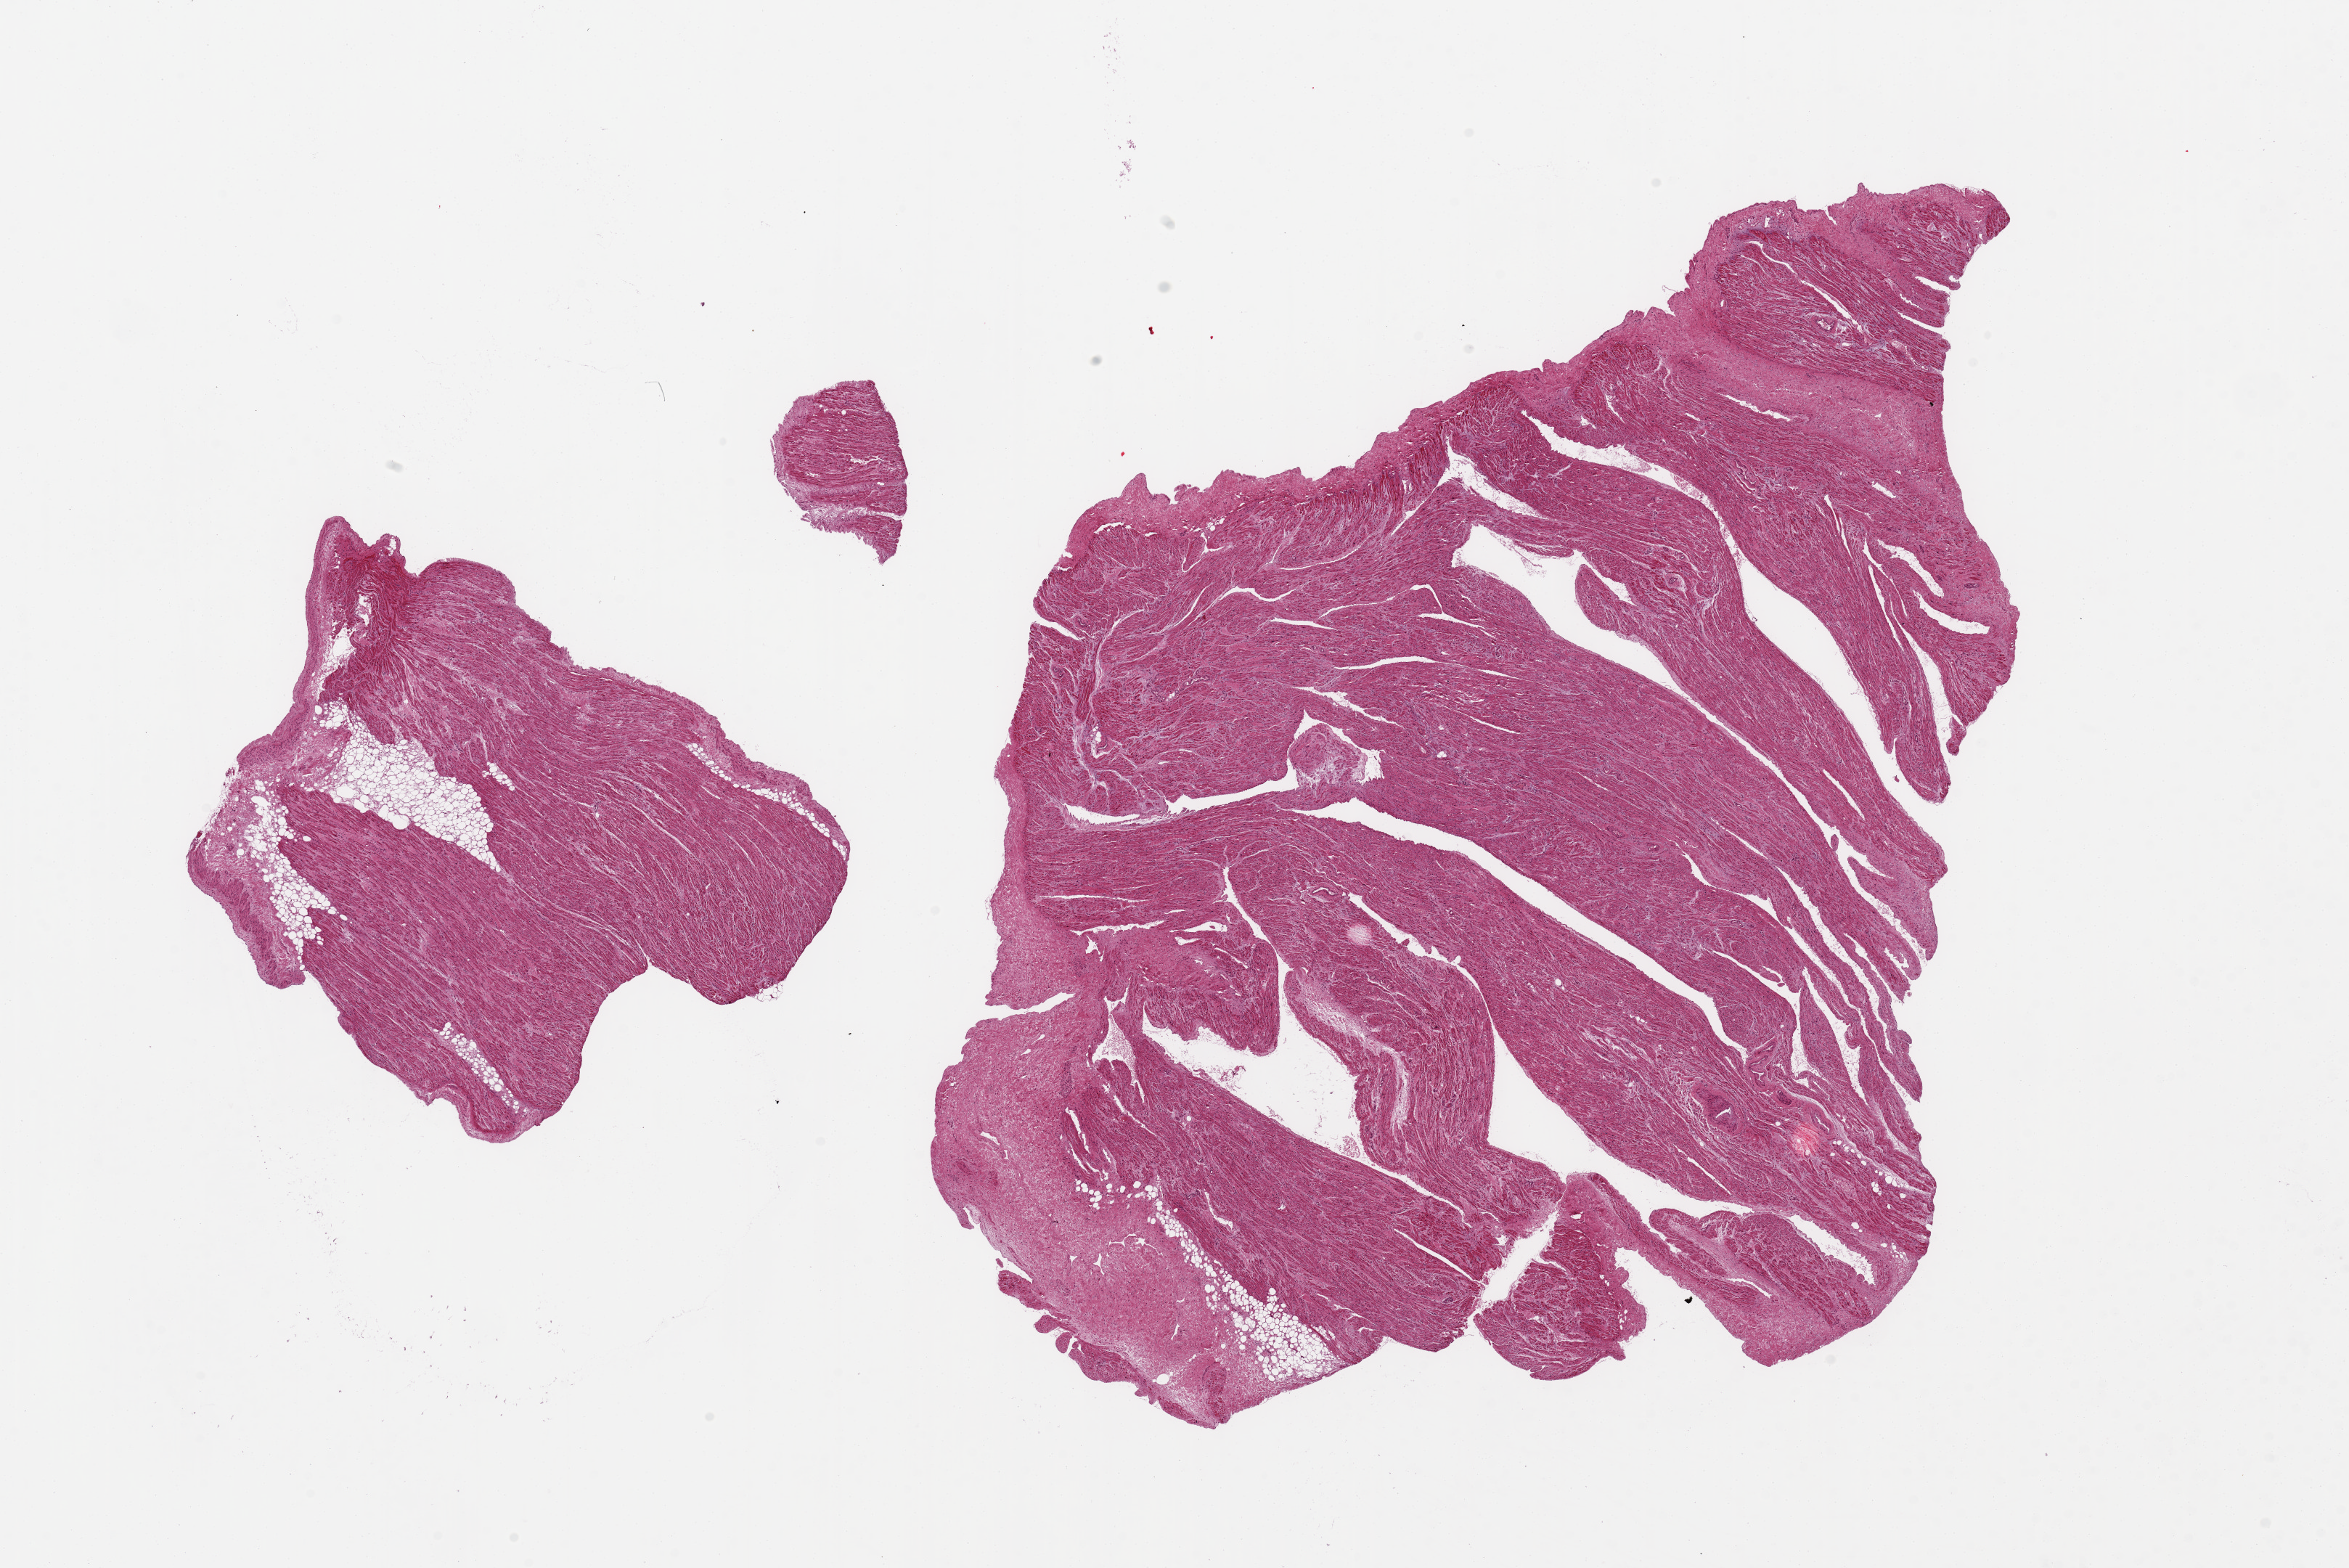
Digitized H&E-stained section, brightfield, a low-resolution overview of the entire scanned area, about 25.6 x 17.1 mm; PAXgene-fixed paraffin-embedded (PFPE) section; section of auricular appendage (target tissue); donor tissue sample. Donor: female.
Reviewer comment on this tissue sample: 2 pieces, 7x5 & 16x12mm.